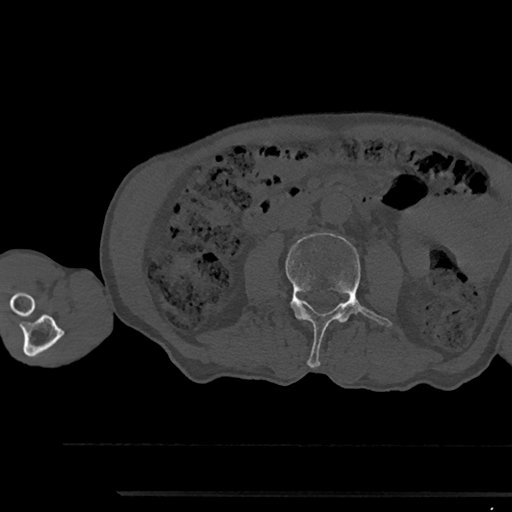
CT including the spine, one axial slice; slice 486 of 797 in the series (ordered by position); 120 kVp; bone window (W 1800 / L 400 HU); 0.5 mm slice thickness; 512 × 512 image matrix, field of view 367 × 367 mm. Male patient, age 79 years. Case-level facts recorded for this patient, not image findings: primary cancer: prostate.
Annotated regions visible in this slice (semi-automatically segmented with operator editing):
- L3 vertebra: bounding box (x1, y1, x2, y2) in pixels: (285, 233, 392, 367)